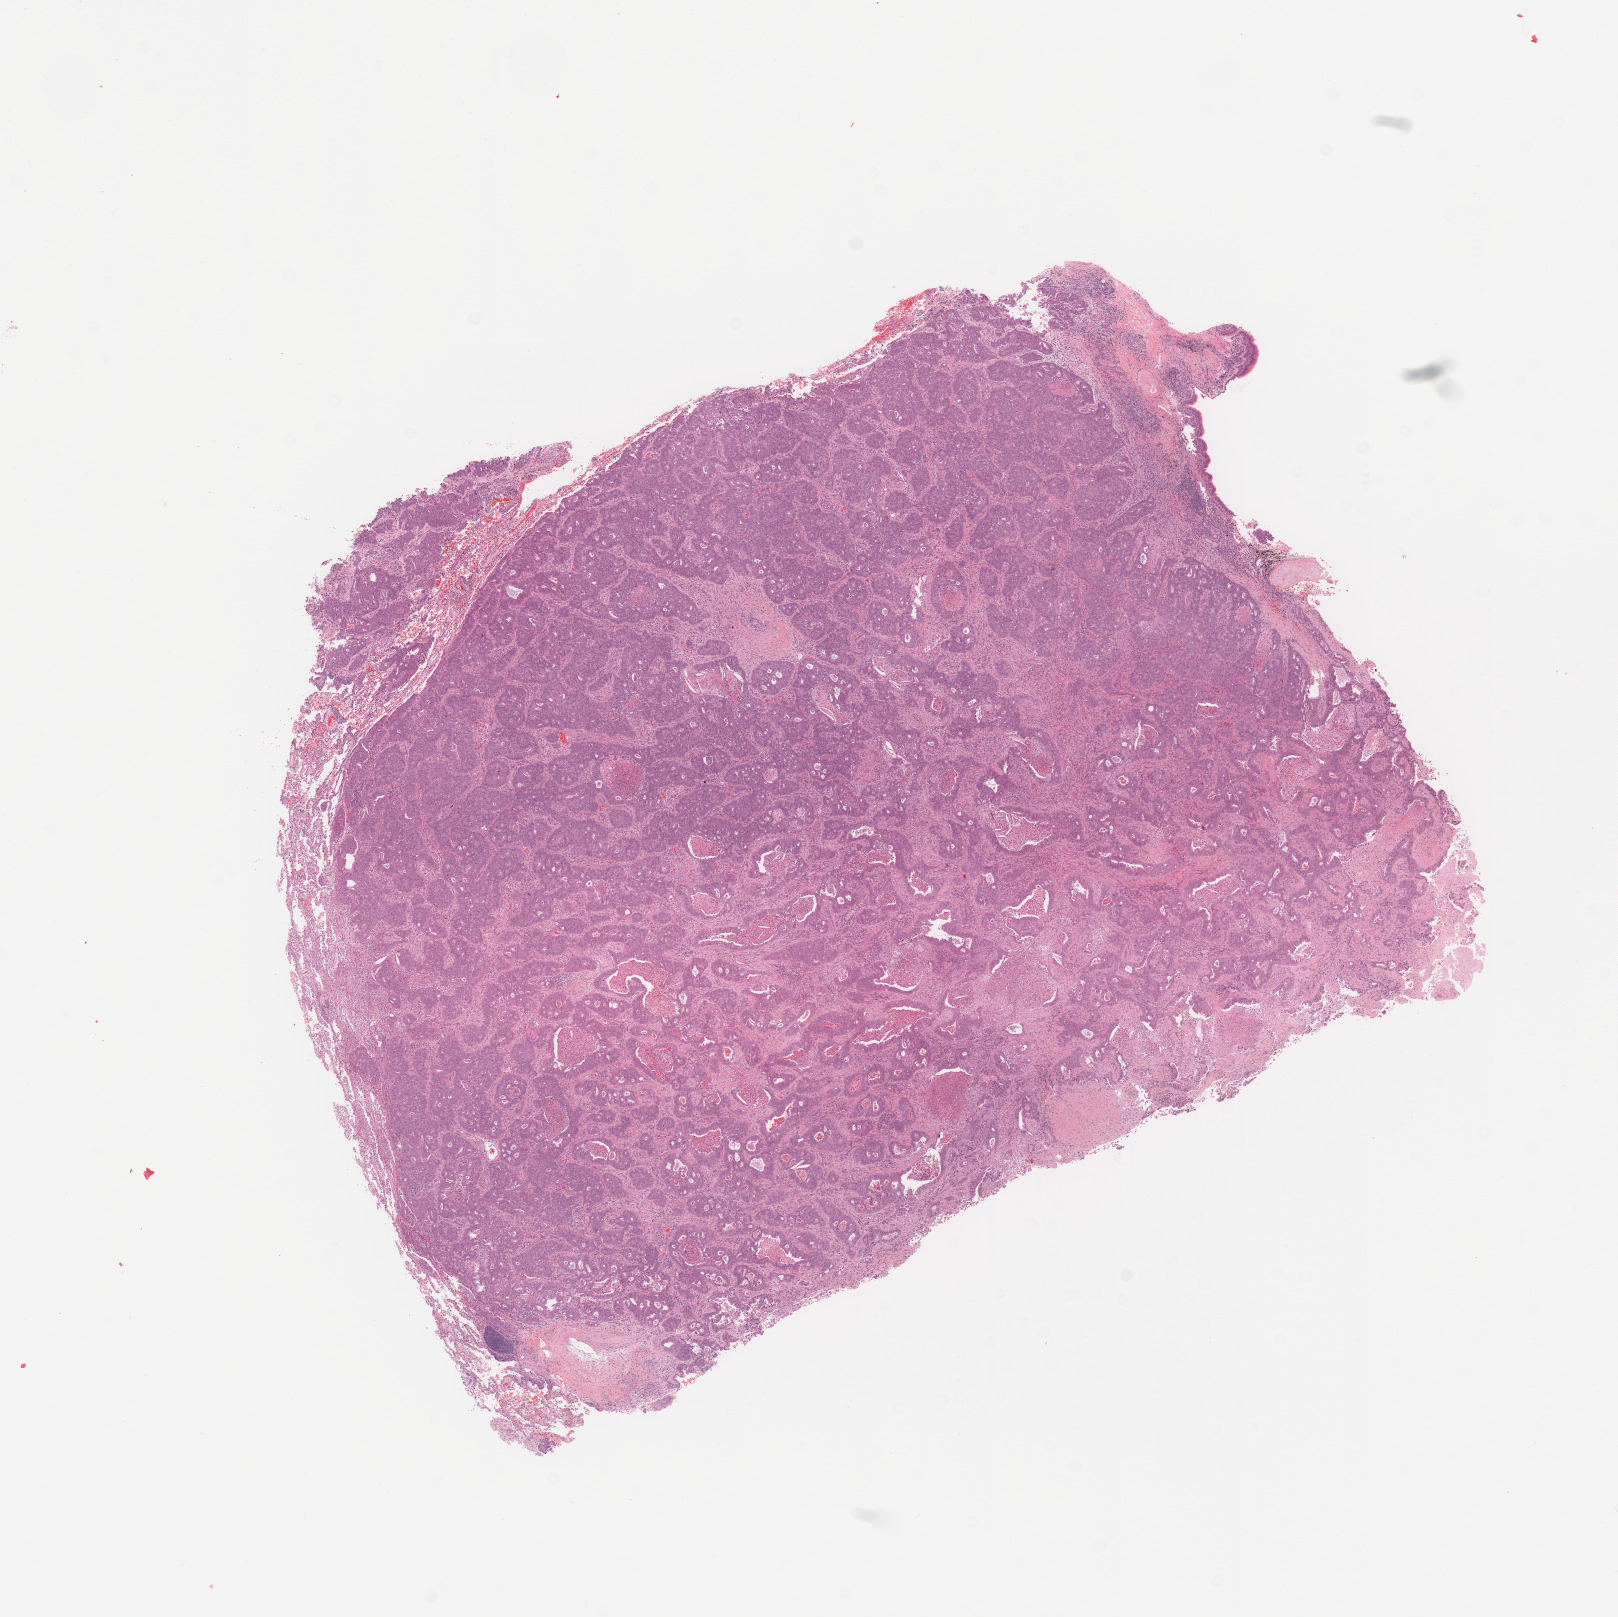
Digitized H&E-stained tissue section (whole slide), low-resolution overview of the scanned area, about 12.8 x 12.8 mm; tumour tissue sample, sampled site: lung. Male, 69 y/o. Histologic grade: G3 (poorly differentiated). Slide review estimates, as recorded: tumour nuclei 80%, necrosis 5%.
AJCC pathologic stage: IV. Diagnosis: Adenocarcinoma, NOS. Primary tumour site (as recorded): right lower lobe.